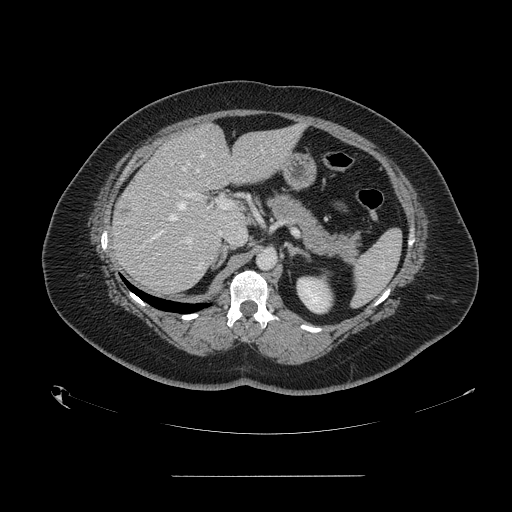
Contrast-enhanced abdominal CT, one axial slice; position 92 of 164 along the scan axis; 120 kVp; intravenous contrast given; soft-tissue window (W 400 / L 40 HU); 512 × 512 image matrix, field of view 495 × 495 mm. Female patient, age 52 years. From the clinical record (not read from this slice): diagnosis: colorectal cancer liver metastases, imaged before liver resection; multiple liver metastases: yes; largest metastasis: 3.5 cm; disease in both lobes: no.
Structures marked on this image (outlined manually by an expert reader):
- hepatic veins: box from (x=148, y=153) to (x=203, y=242) px
- liver: (x=112, y=125)–(x=300, y=293)
- planned liver remnant (the part of the liver to remain after resection): (x=176, y=124)–(x=300, y=226)
- portal vein (with intrahepatic branches): (x=178, y=190)–(x=234, y=243)
- liver metastasis: (x=121, y=209)–(x=130, y=215)